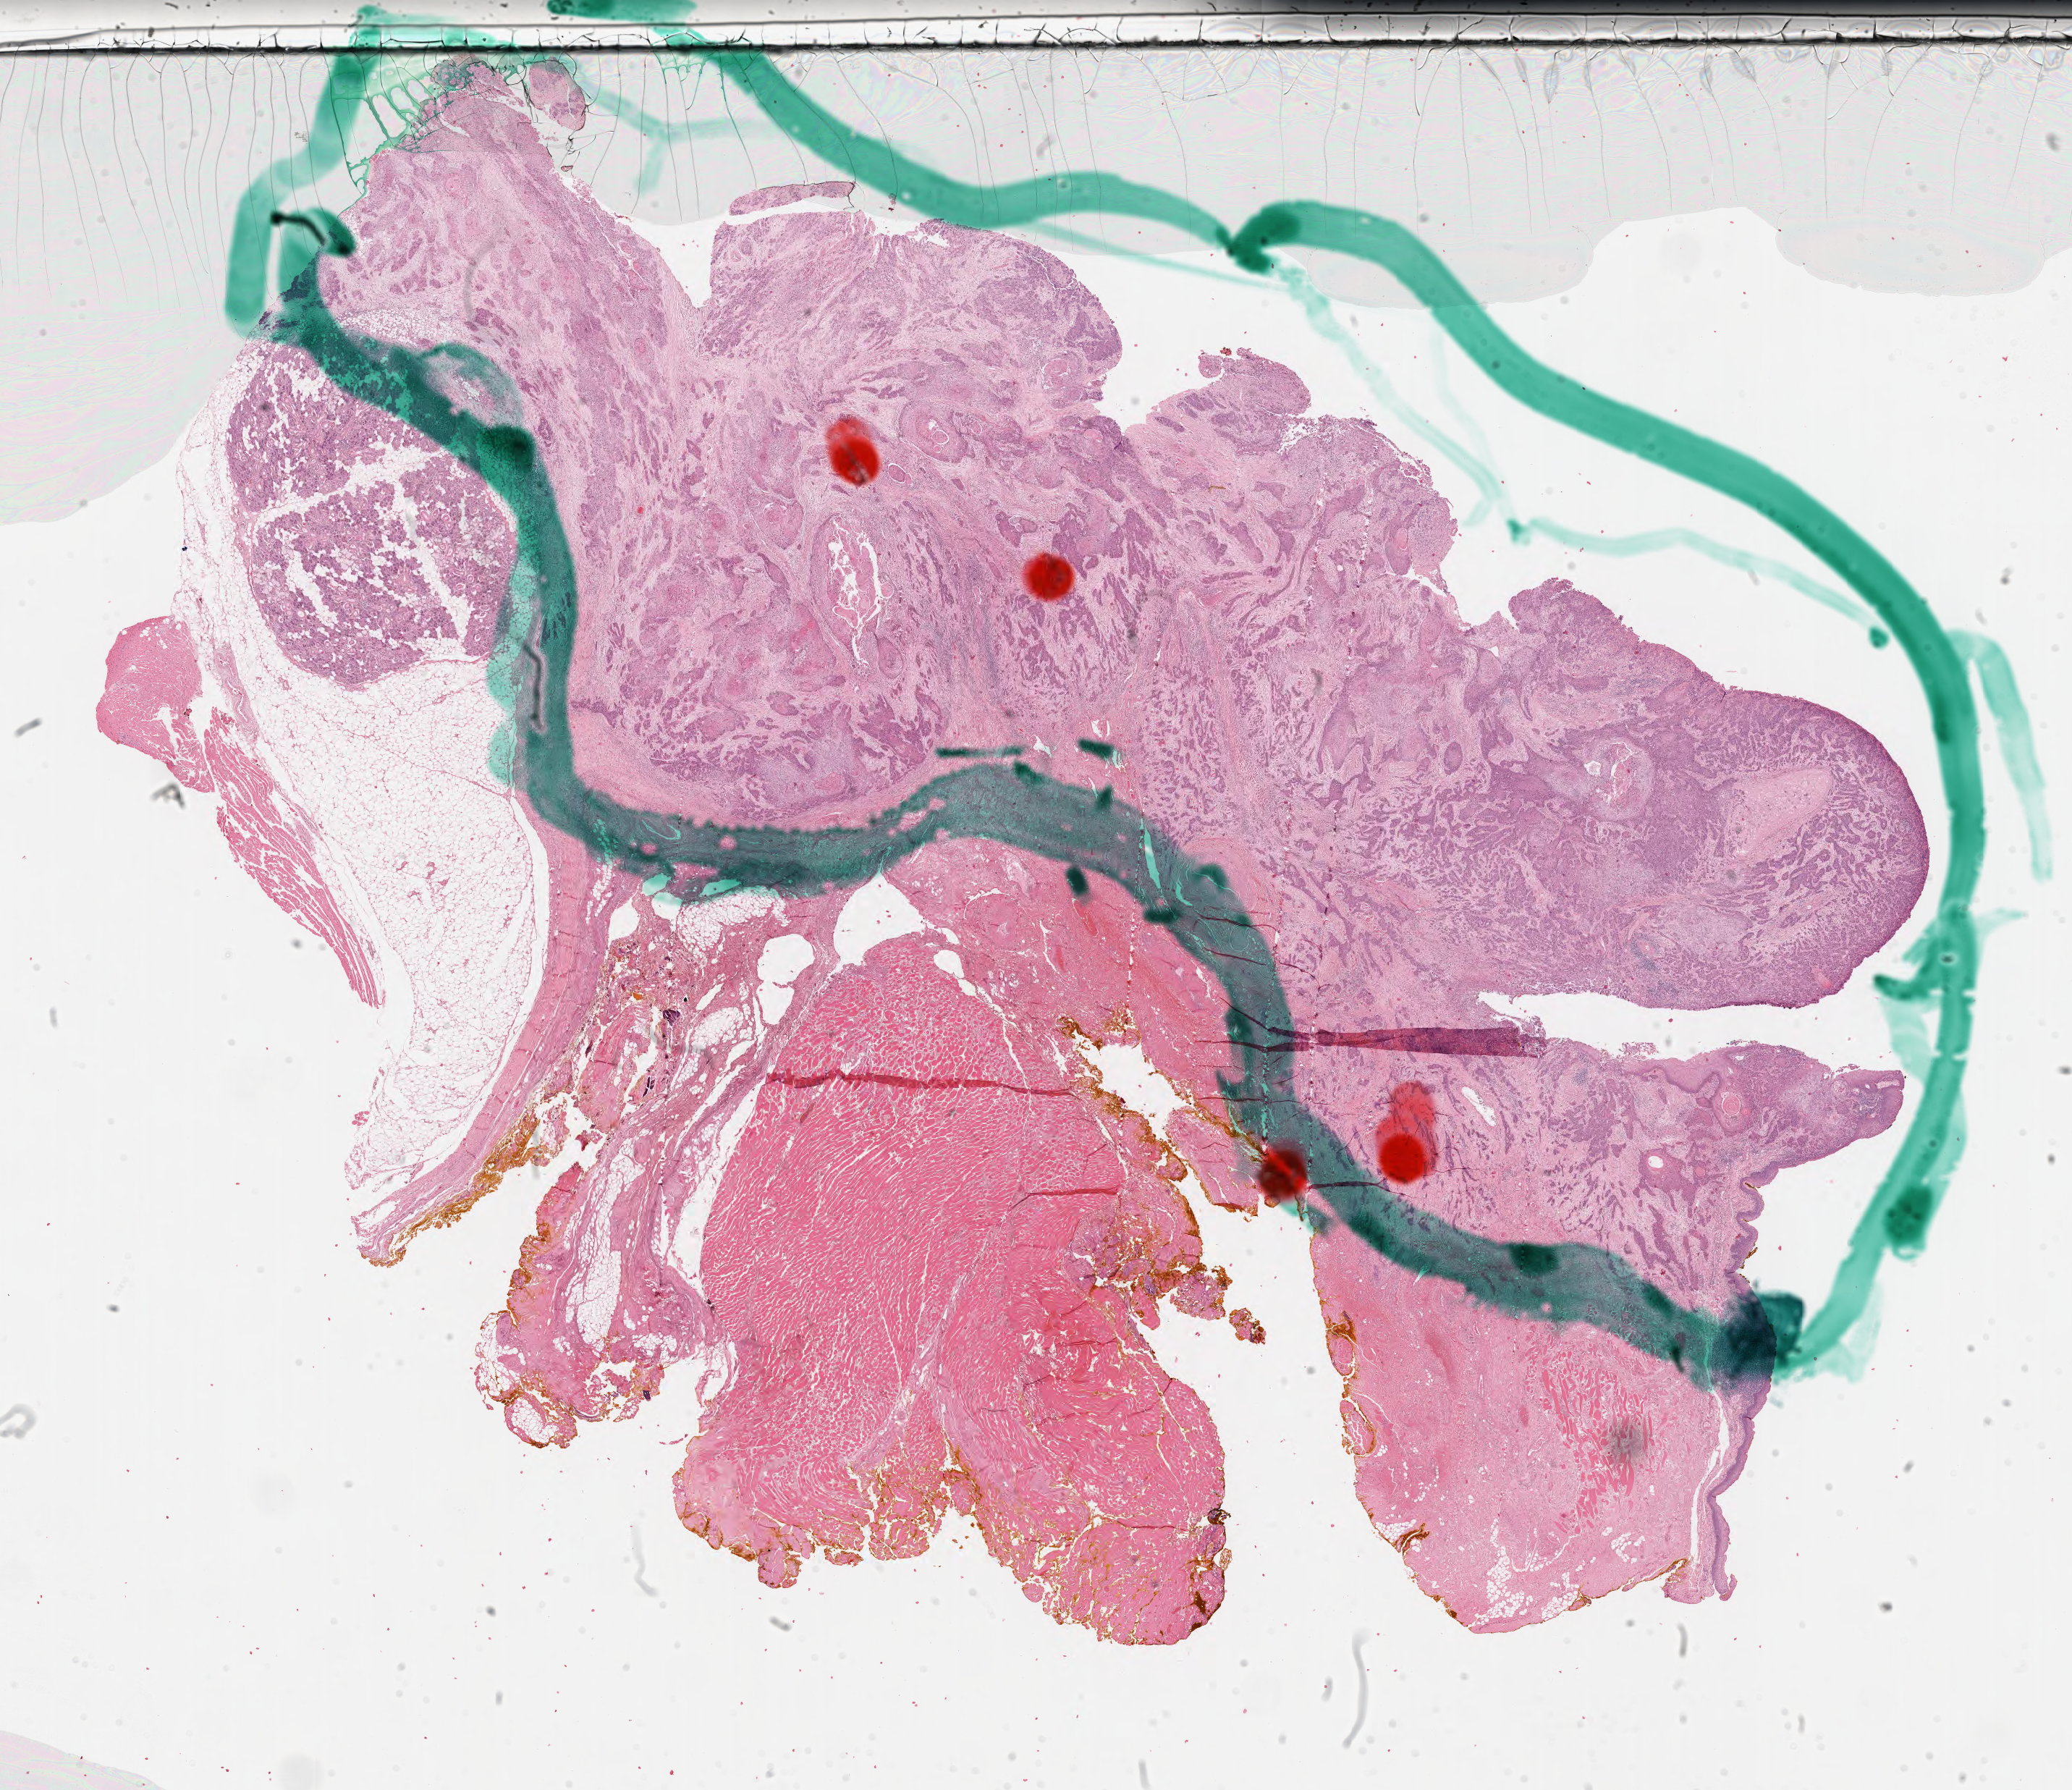
Whole-slide histology image, Hematoxylin and eosin (H&E) stained — shown as a low-resolution overview of the whole scanned area (about 22.5 x 19.5 mm, from a 40x scan); FFPE section; primary tumour sample from the head and neck. Male, age 67 years at initial diagnosis.
Diagnosis: Squamous cell carcinoma, NOS (tonsil, NOS).